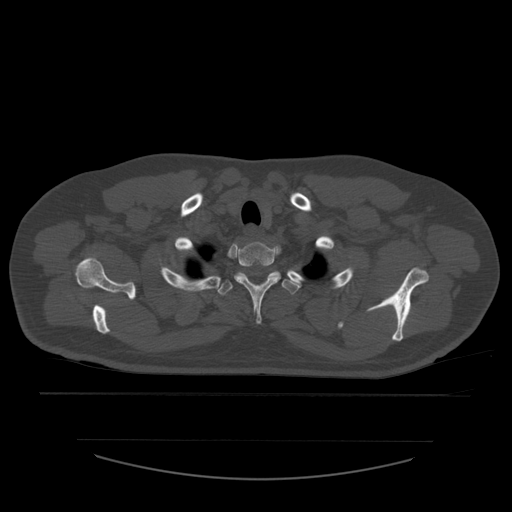
CT including the spine, one axial slice. Reconstruction kernel STANDARD. 120 kVp. Bone window (W 1800 / L 400 HU). 512 × 512 image matrix. Patient age 44 years. From the clinical record (not read from this slice): primary cancer: soft tissue sarcoma.
Annotated regions visible in this slice (semi-automatic segmentation, software-assisted and operator-edited):
- T1 vertebra: bounding box (x1, y1, x2, y2) in pixels: (235, 242, 281, 324)
- T2 vertebra: (217, 271, 302, 296)